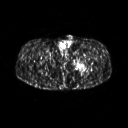
FDG PET of an extremity soft-tissue mass (from a PET/CT study), one axial slice. Position 260 of 267 along the scan axis. 128 × 128 image matrix, field of view 500 × 500 mm. Male patient, age 27 years. Case-level facts recorded for this patient, not image findings: histological type: extraskeletal osteosarcoma; grade: high; site of the primary tumour: left adductur.
Outlined on this slice (expert contour drawn on MRI and transferred to this co-registered scan by the dataset authors):
- gross tumour volume (mass): bounding box [x1, y1, x2, y2] px = [71, 52, 96, 75]